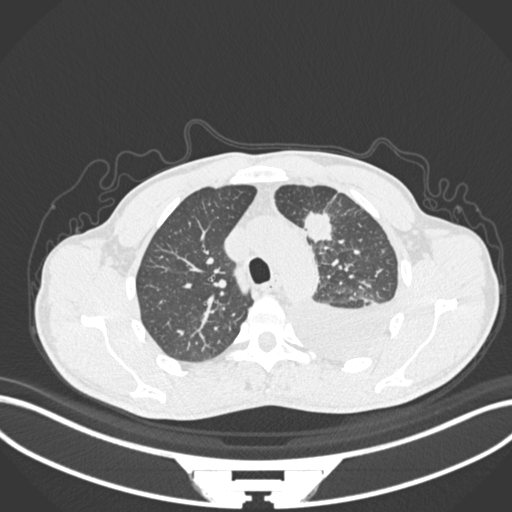
Chest CT, one axial slice; position 163 of 244 along the scan axis; lung window (W 1500 / L -600 HU); 1 mm slice thickness; 512 × 512 image matrix. Patient: male, 49 years. From the clinical record (not read from this slice): clinical TNM (as recorded): T1c N1 M1.
Annotated regions visible in this slice (bounding box drawn by a radiologist):
- lung tumour (recorded histology: adenocarcinoma): box from (x=305, y=206) to (x=337, y=245) px